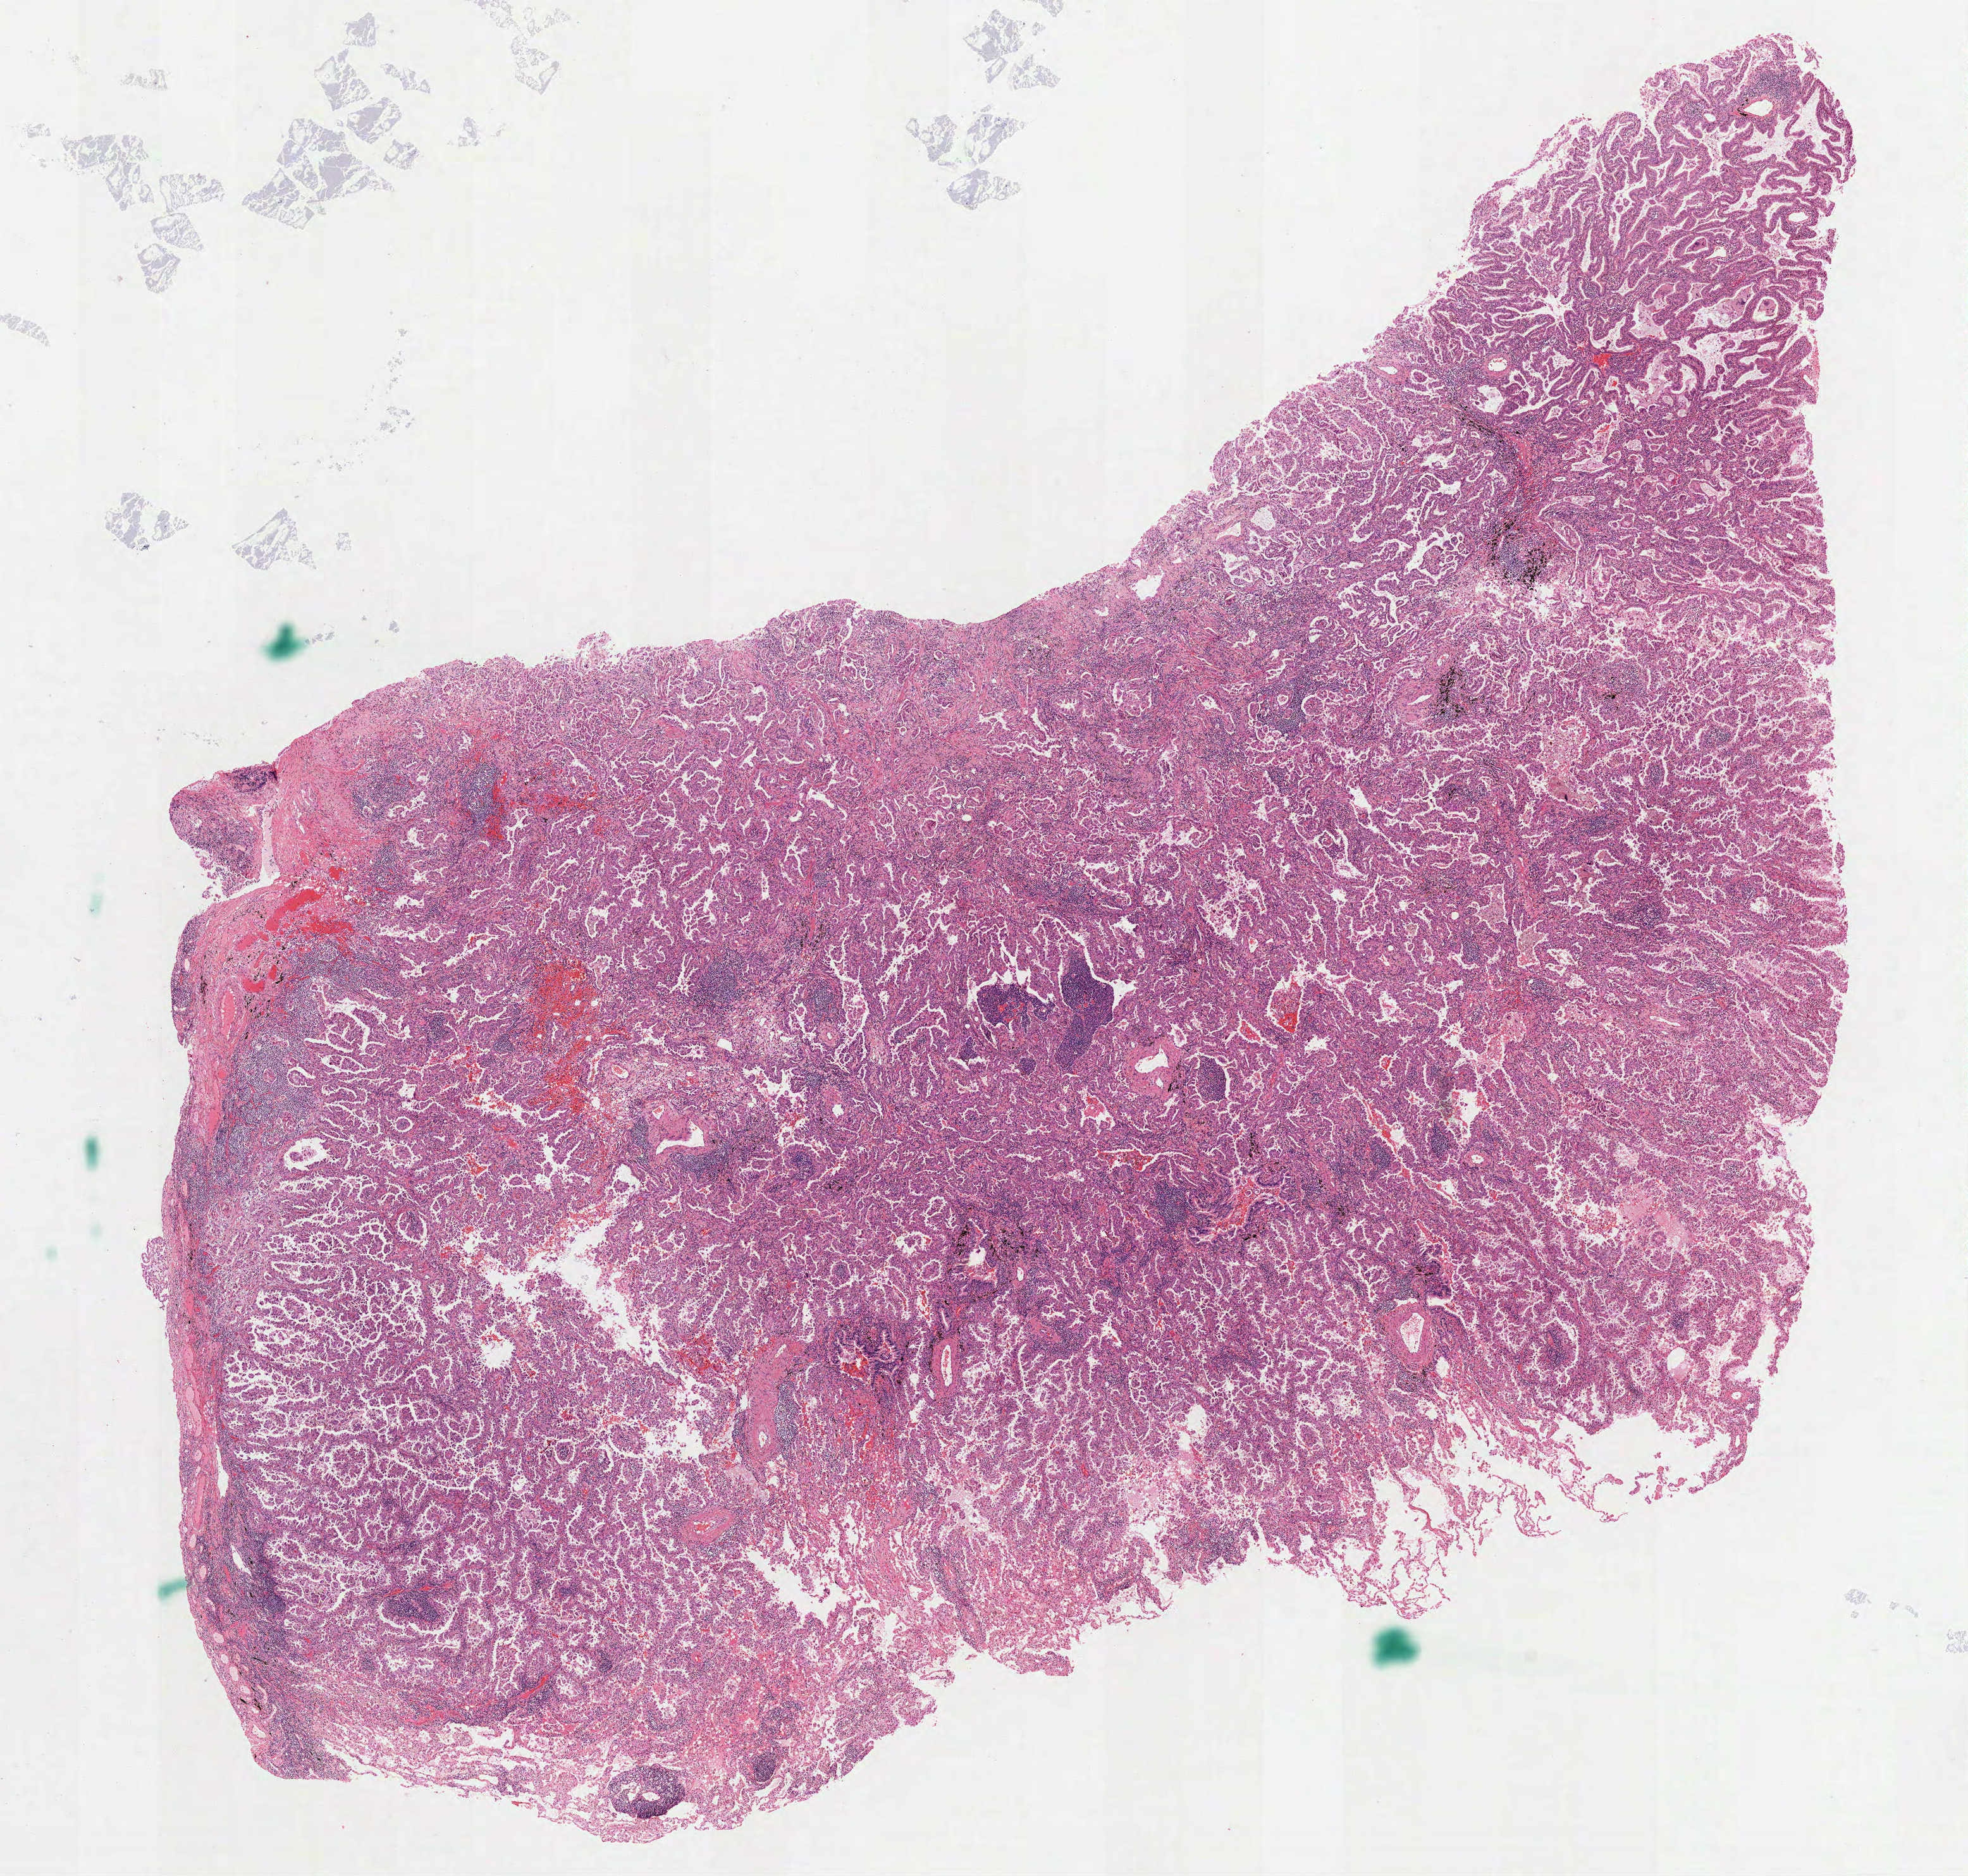
Hematoxylin and eosin (H&E) stained whole-slide image, whole scanned area (about 12.5 x 12.0 mm) shown as a low-resolution overview, formalin-fixed paraffin-embedded (FFPE) diagnostic section, sample: primary tumour, lung. Male, age 75 years at initial diagnosis.
Laterality: right. Diagnosis: Adenocarcinoma, NOS (lower lobe, lung). TNM: T1 NX M0. AJCC pathologic stage: IA.